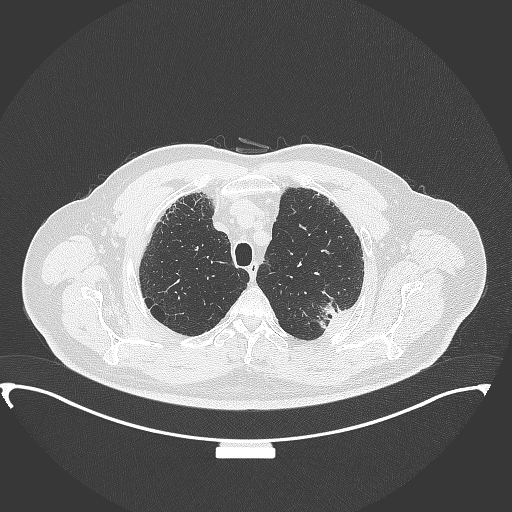
Chest CT, one axial slice. Position 298 of 350 along the scan axis. 120 kVp. Lung window (W 1500 / L -600 HU). 1 mm slice thickness. 512 × 512 image matrix, field of view 459 × 459 mm. Male patient, age 64 years. From the clinical record (not read from this slice): clinical TNM (as recorded): T1c N1 M1.
Outlined on this slice (bounding box drawn by a radiologist):
- lung tumour (recorded histology: adenocarcinoma): box from (x=312, y=292) to (x=346, y=334) px